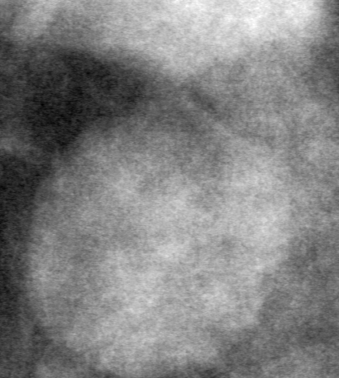
Cropped region of a digitized screen-film mammogram centred on a radiologist-marked abnormality; left breast; CC view; BI-RADS breast density category 3 (scale 1–4).
Finding: mass, shape round, margins circumscribed; BI-RADS assessment category 4; subtlety rating 4 on a 1 (subtle) to 5 (obvious) scale; pathology (as recorded): benign.